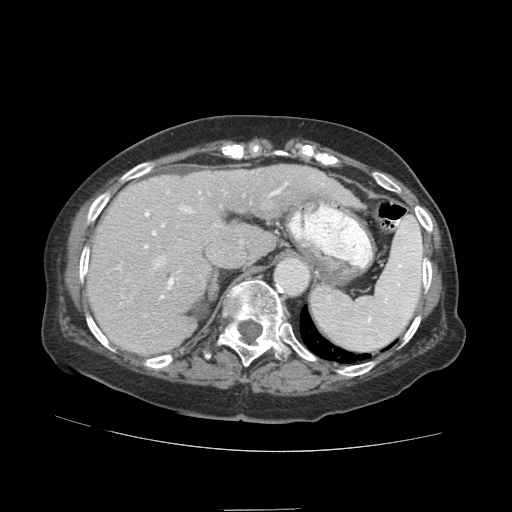
Contrast-enhanced abdominal CT (liver protocol), one axial slice. Slice 65 of 89 in the series (ordered by position). Reconstruction kernel STANDARD. 140 kVp. Soft-tissue window (W 400 / L 40 HU). 512 × 512 image matrix, field of view 360 × 360 mm. Case-level facts recorded for this patient, not image findings: diagnosis: hepatocellular carcinoma (patient treated with transarterial chemoembolisation; whether this scan precedes or follows treatment is not stated here); TNM stage (as recorded): Stage-II; Child-Pugh class: A; tumour differentiation: moderately differentiated; tumour nodularity: multinodular.
Outlined on this slice (semi-automatic segmentation, software-assisted and operator-edited):
- liver parenchyma outside the tumour (the mass and vessels are separate outlines, so this box may not span the whole liver): bounding box [x1, y1, x2, y2] px = [88, 166, 297, 354]
- liver vessels: [117, 172, 289, 306]